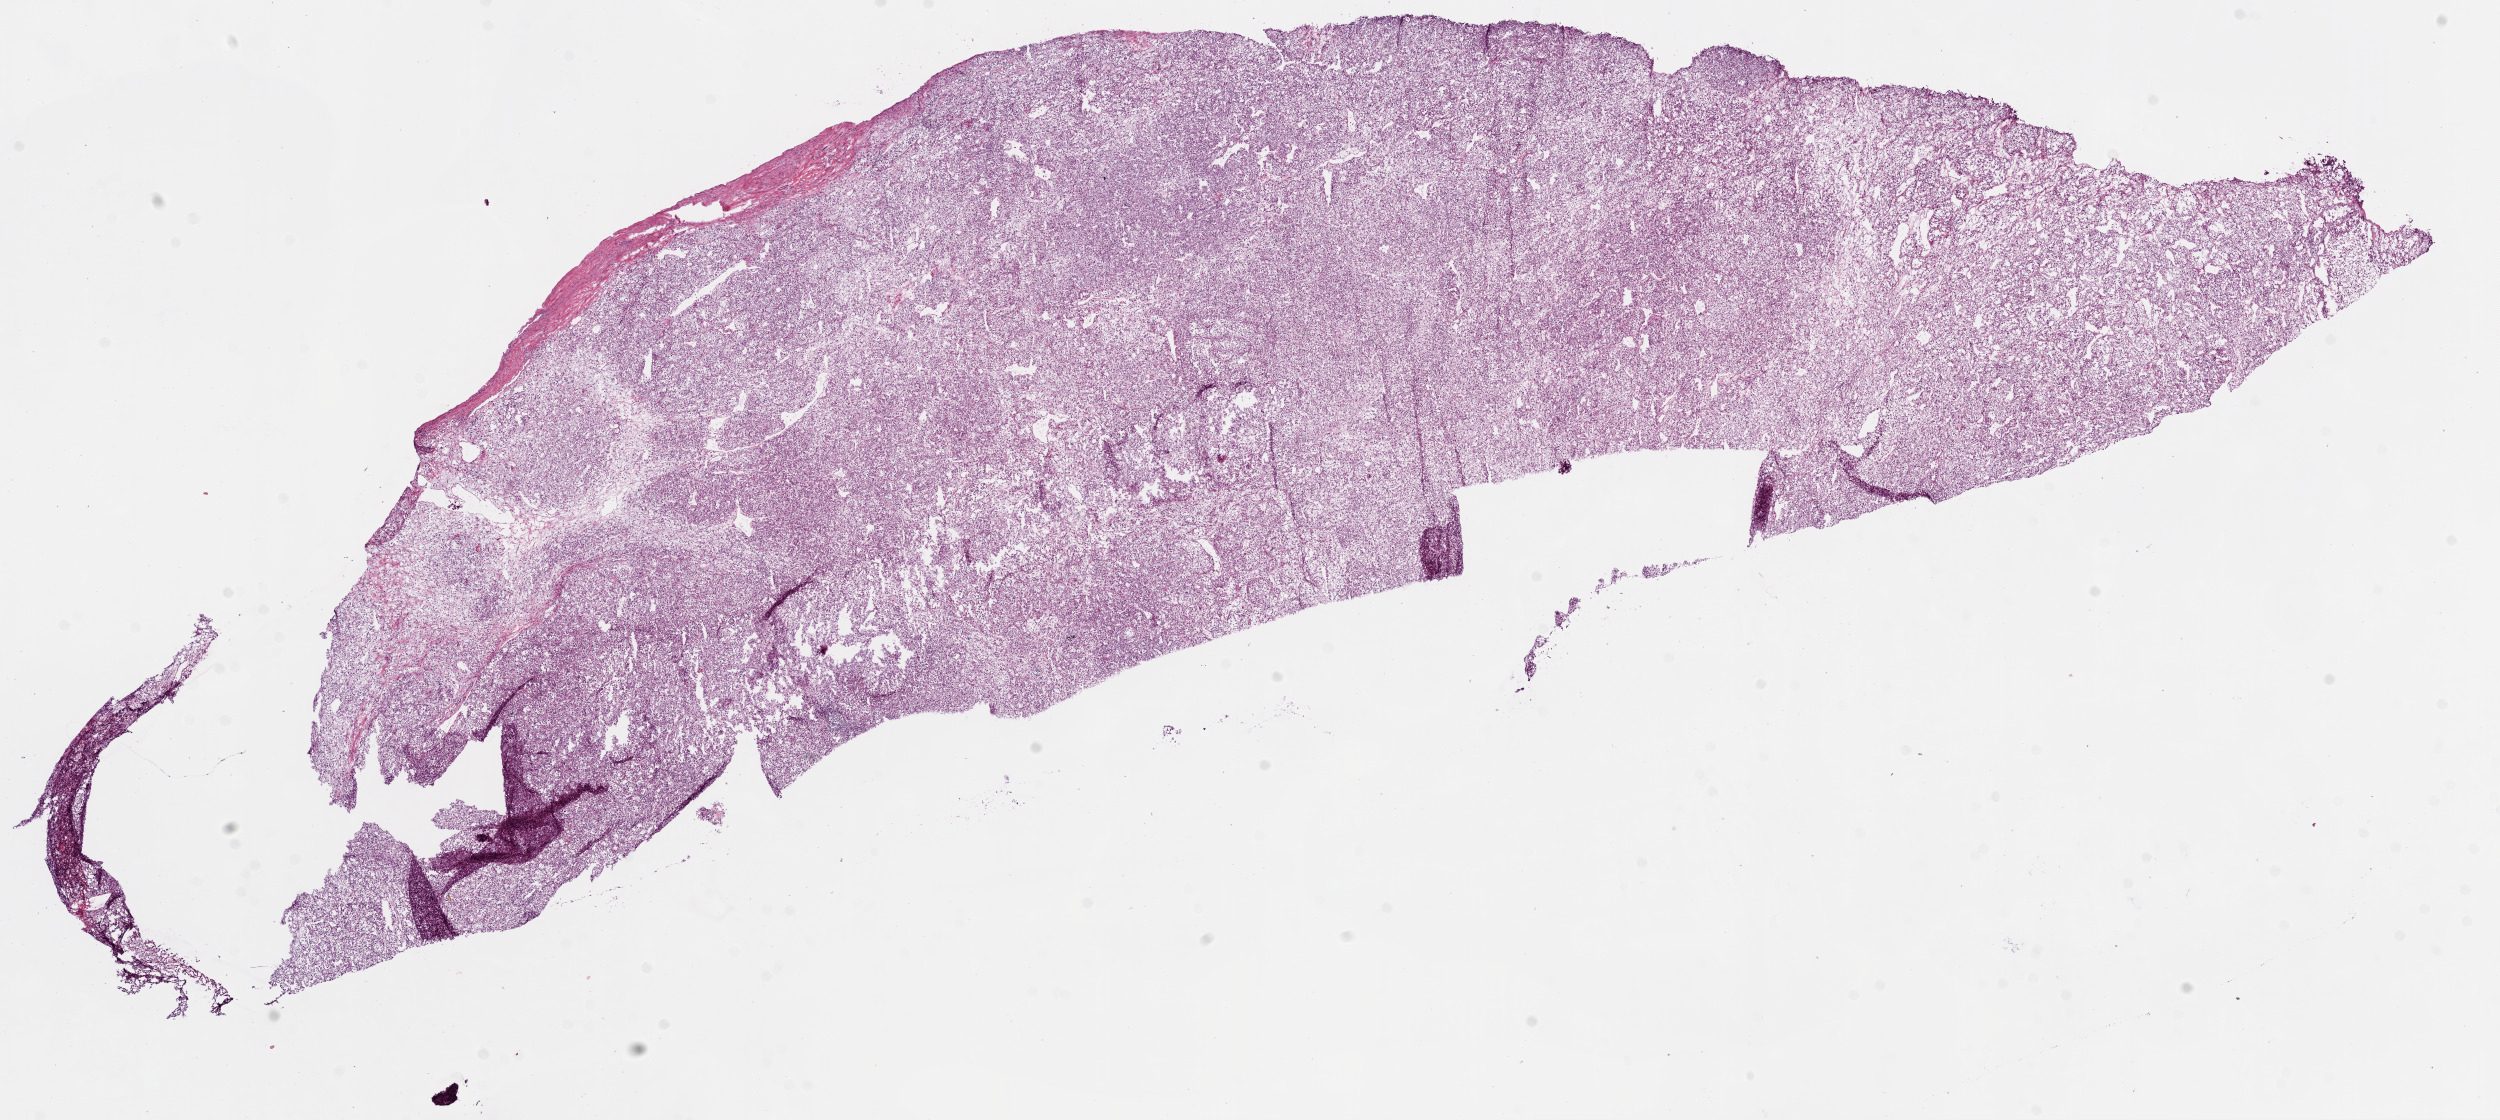
Digitized H&E-stained tissue section (whole slide) — a low-resolution overview of the entire scanned area, about 20.1 x 9.0 mm (acquisition: 20x scan); frozen section from the bottom of the tissue portion; sample: primary tumour, kidney. Female patient; age at initial diagnosis 69 years. Histologic grade: G3 (poorly differentiated). Composition of this section per pathologist review: tumour cells 95%, tumour nuclei 90%, normal cells 0%, stromal cells 5%, necrosis 0%.
TNM: T1b N0 M0. Histologic diagnosis: Clear cell adenocarcinoma, NOS. AJCC pathologic stage: I.